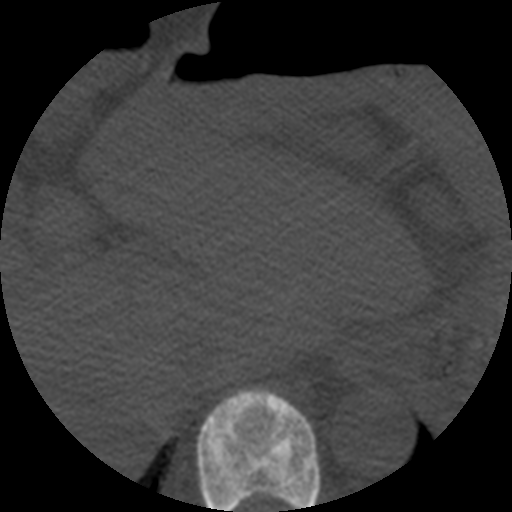
CT including the spine, one axial slice. Slice 263 of 508 in the series (ordered by position). 120 kVp. Bone window (W 1800 / L 400 HU). 1.25 mm slice thickness. 512 × 512 image matrix, field of view 160 × 160 mm. Patient age 57 years. Case-level facts recorded for this patient, not image findings: primary cancer: prostate.
Structures marked on this image (semi-automatically segmented with operator editing):
- T10 vertebra: bounding box [x1, y1, x2, y2] px = [196, 388, 321, 512]